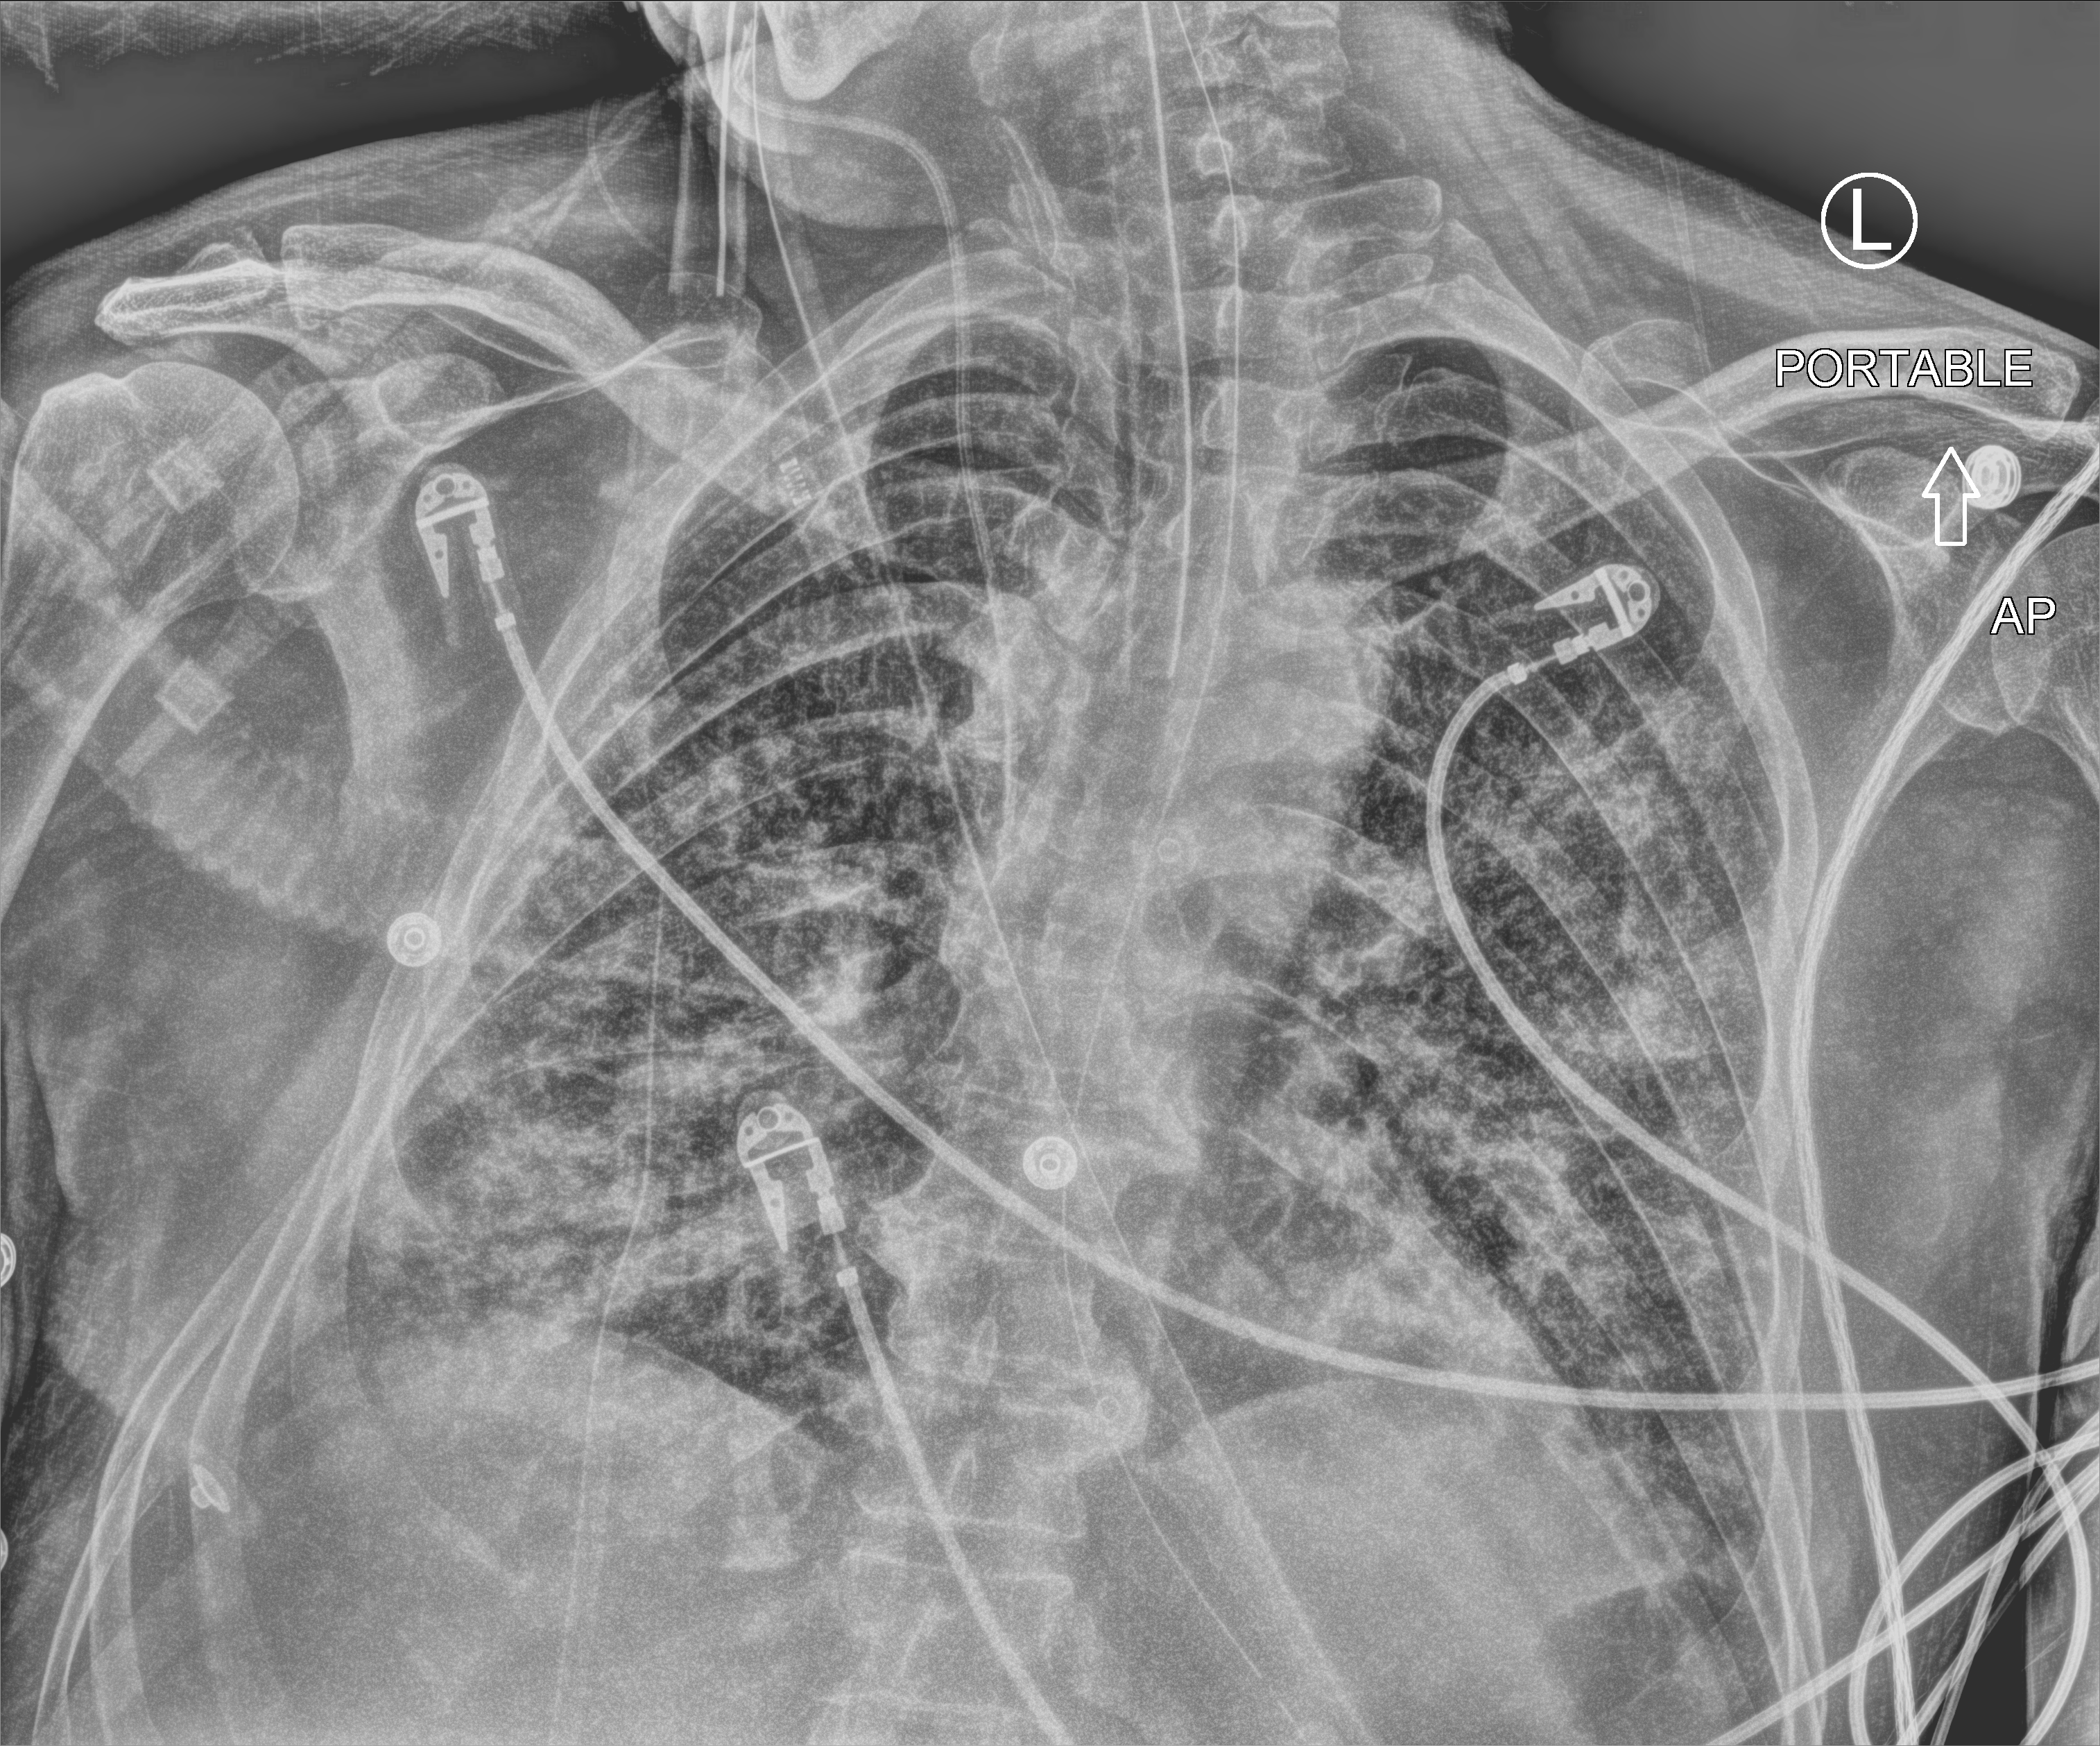
Bedside chest radiograph (computed radiography), anteroposterior (AP) projection. Patient hospitalised with COVID-19; male, aged 60–74 years.
Admission-level facts for this patient (not findings on this image; timing relative to this image not recorded): admitted to intensive care during this hospital stay: yes.